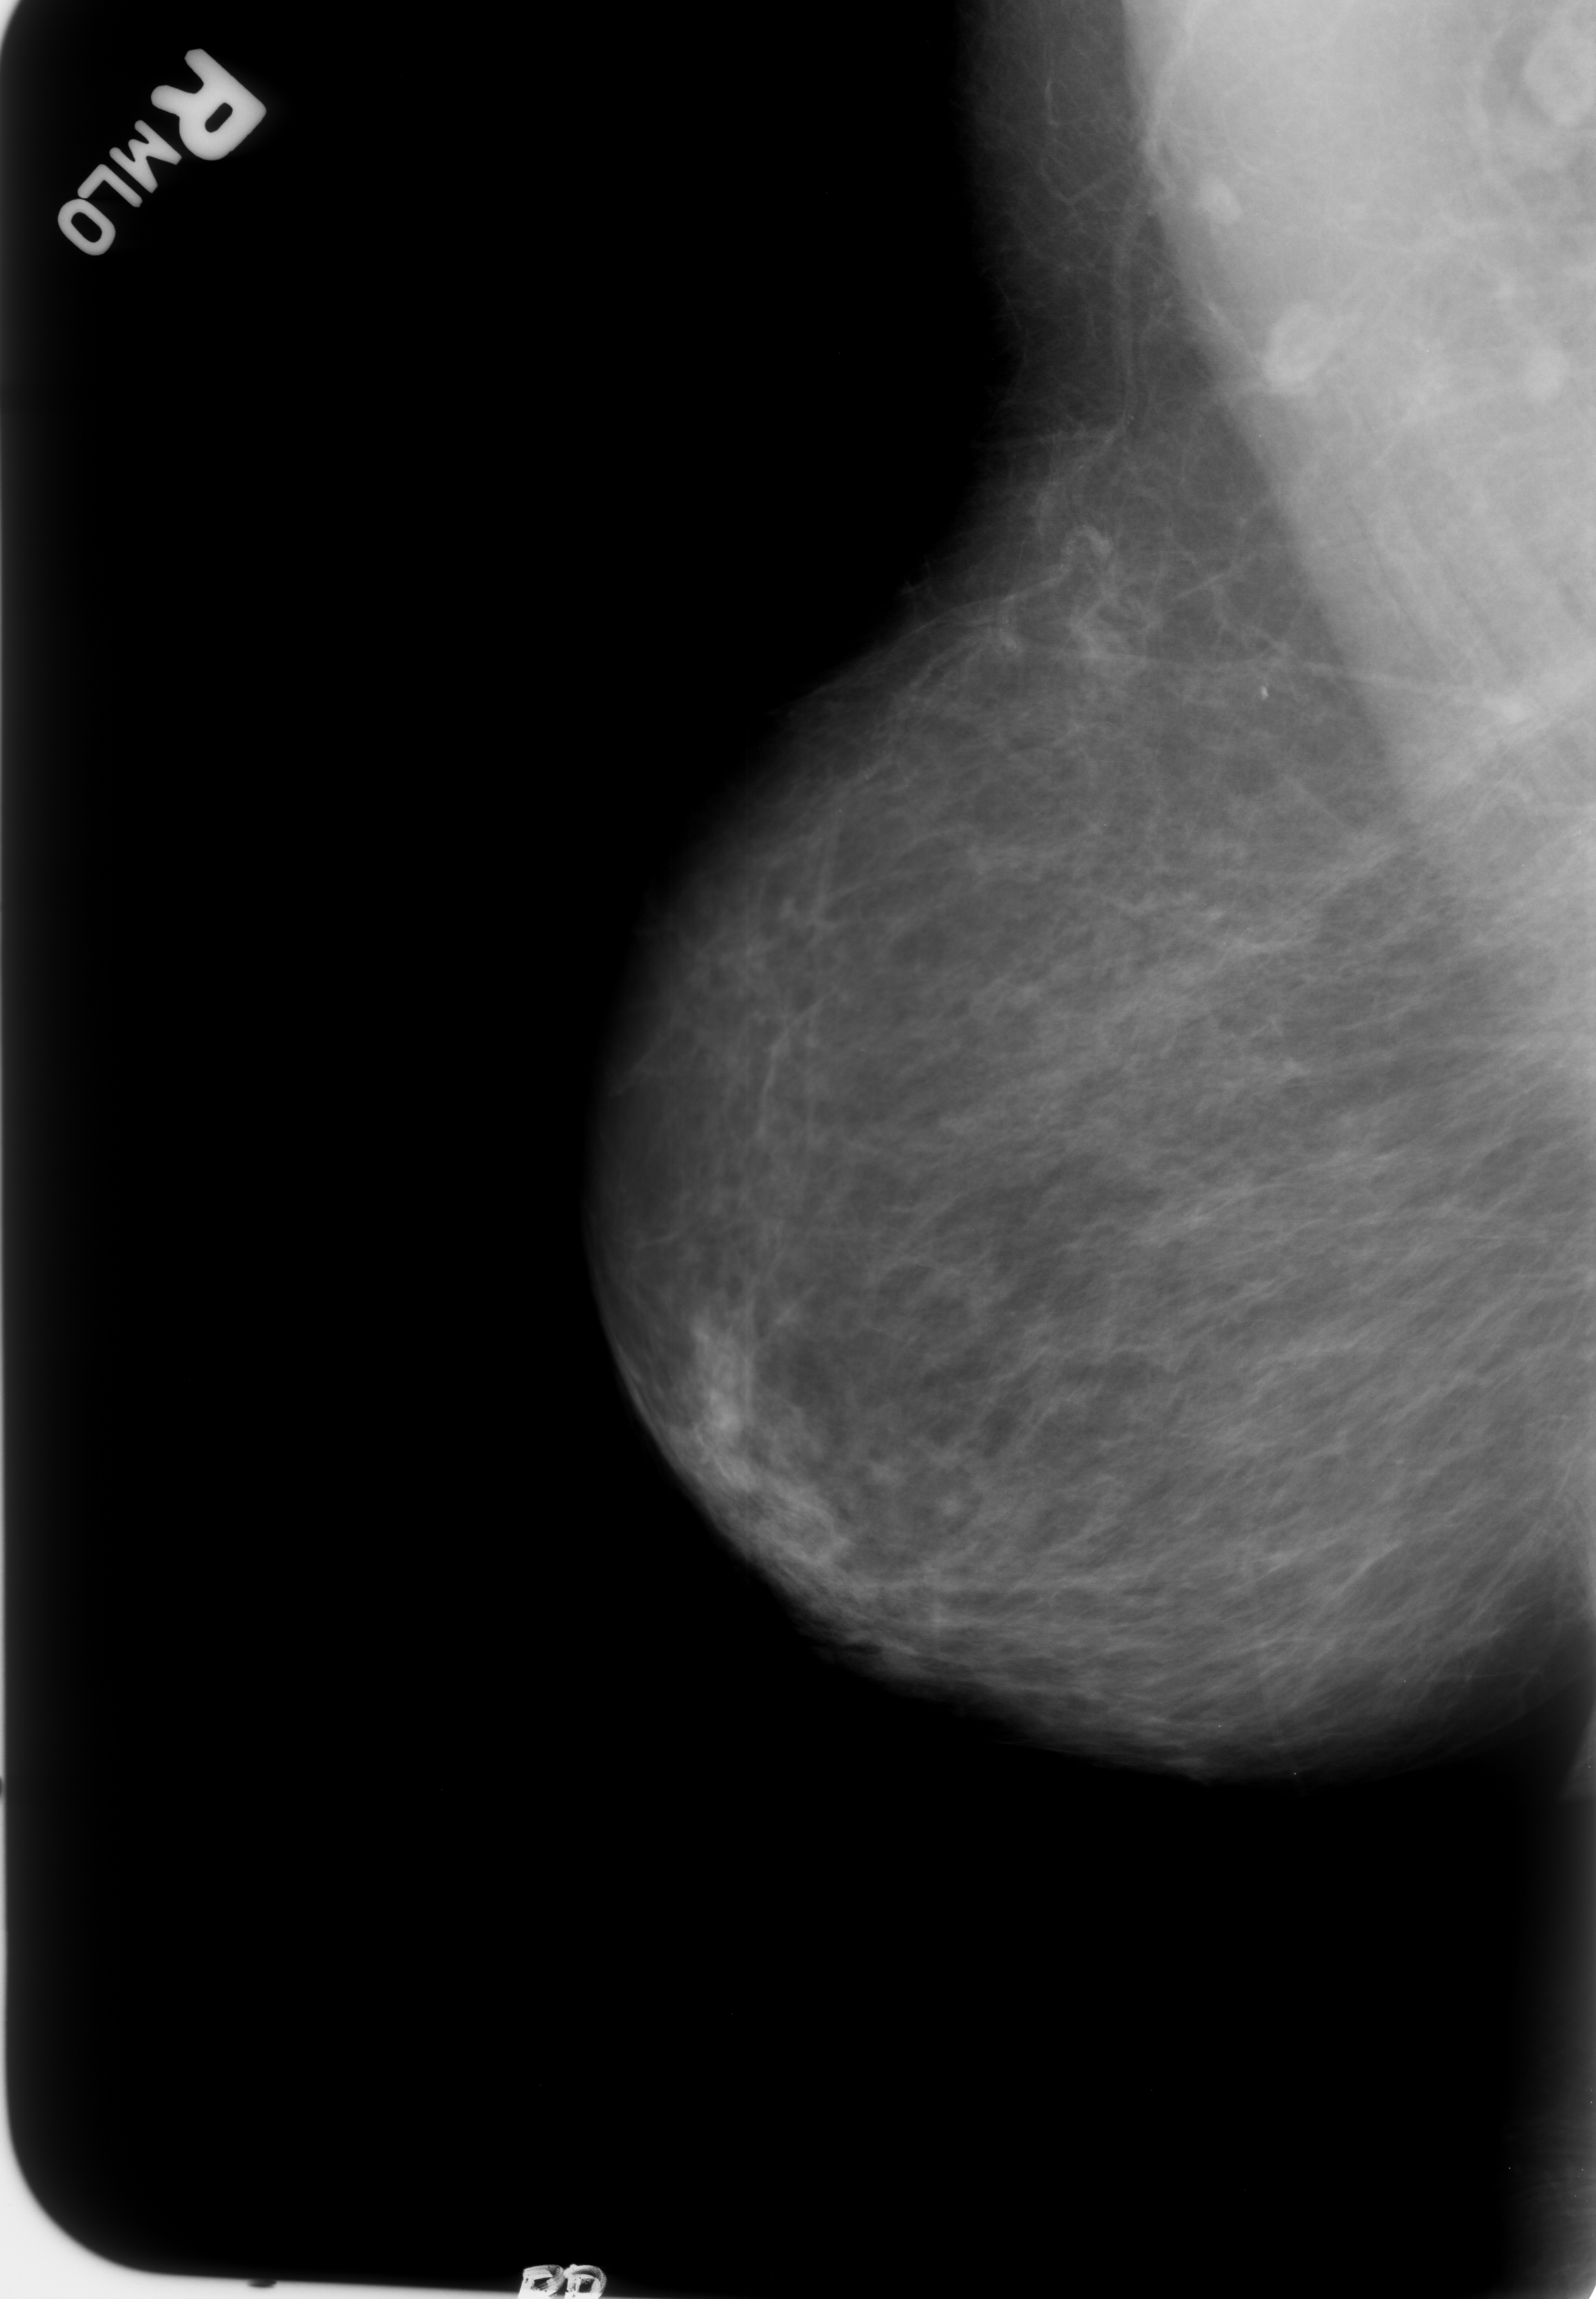
Scanned film-screen mammogram, right breast, mediolateral oblique (MLO) view, BI-RADS breast density category 1 (scale 1–4).
Marked abnormality: calcifications, morphology coarse; BI-RADS assessment category 2; benign without callback (not worked up further).